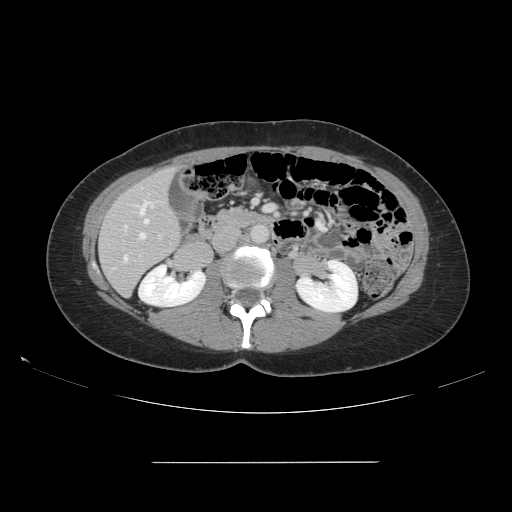
Contrast-enhanced abdominal CT, one axial slice; 120 kVp; intravenous contrast given; soft-tissue window (W 400 / L 40 HU); 2.5 mm slice thickness; 512 × 512 image matrix, field of view 421 × 421 mm. Female patient, age 46 years. Case-level facts recorded for this patient, not image findings: diagnosis: colorectal cancer liver metastases, imaged before liver resection; multiple liver metastases: yes; largest metastasis: 3 cm.
Annotated regions visible in this slice (outlined manually by an expert reader):
- hepatic veins: bounding box [x1, y1, x2, y2] px = [124, 201, 153, 262]
- liver: [99, 168, 181, 295]
- planned liver remnant (the part of the liver to remain after resection): [99, 168, 181, 295]
- portal vein (with intrahepatic branches): [159, 235, 162, 239]